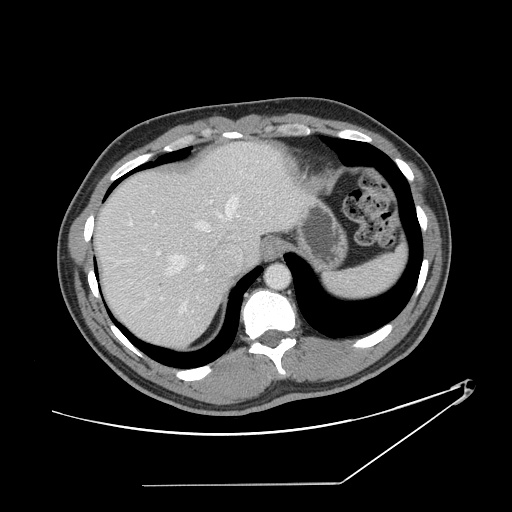
Contrast-enhanced abdominal CT, one axial slice; position 118 of 152 along the scan axis; 120 kVp; soft-tissue window (W 400 / L 40 HU); 2.5 mm slice thickness; 512 × 512 image matrix, field of view 432 × 432 mm. Male patient, age 45 years. Case-level facts recorded for this patient, not image findings: diagnosis: colorectal cancer liver metastases, imaged before liver resection; multiple liver metastases: no; largest metastasis: 1 cm; chemotherapy before resection: yes.
Outlined on this slice (expert manual segmentation):
- hepatic veins: box from (x=111, y=194) to (x=240, y=313) px
- liver: (x=97, y=144)–(x=305, y=348)
- planned liver remnant (the part of the liver to remain after resection): (x=98, y=166)–(x=233, y=348)
- portal vein (with intrahepatic branches): (x=157, y=252)–(x=208, y=325)